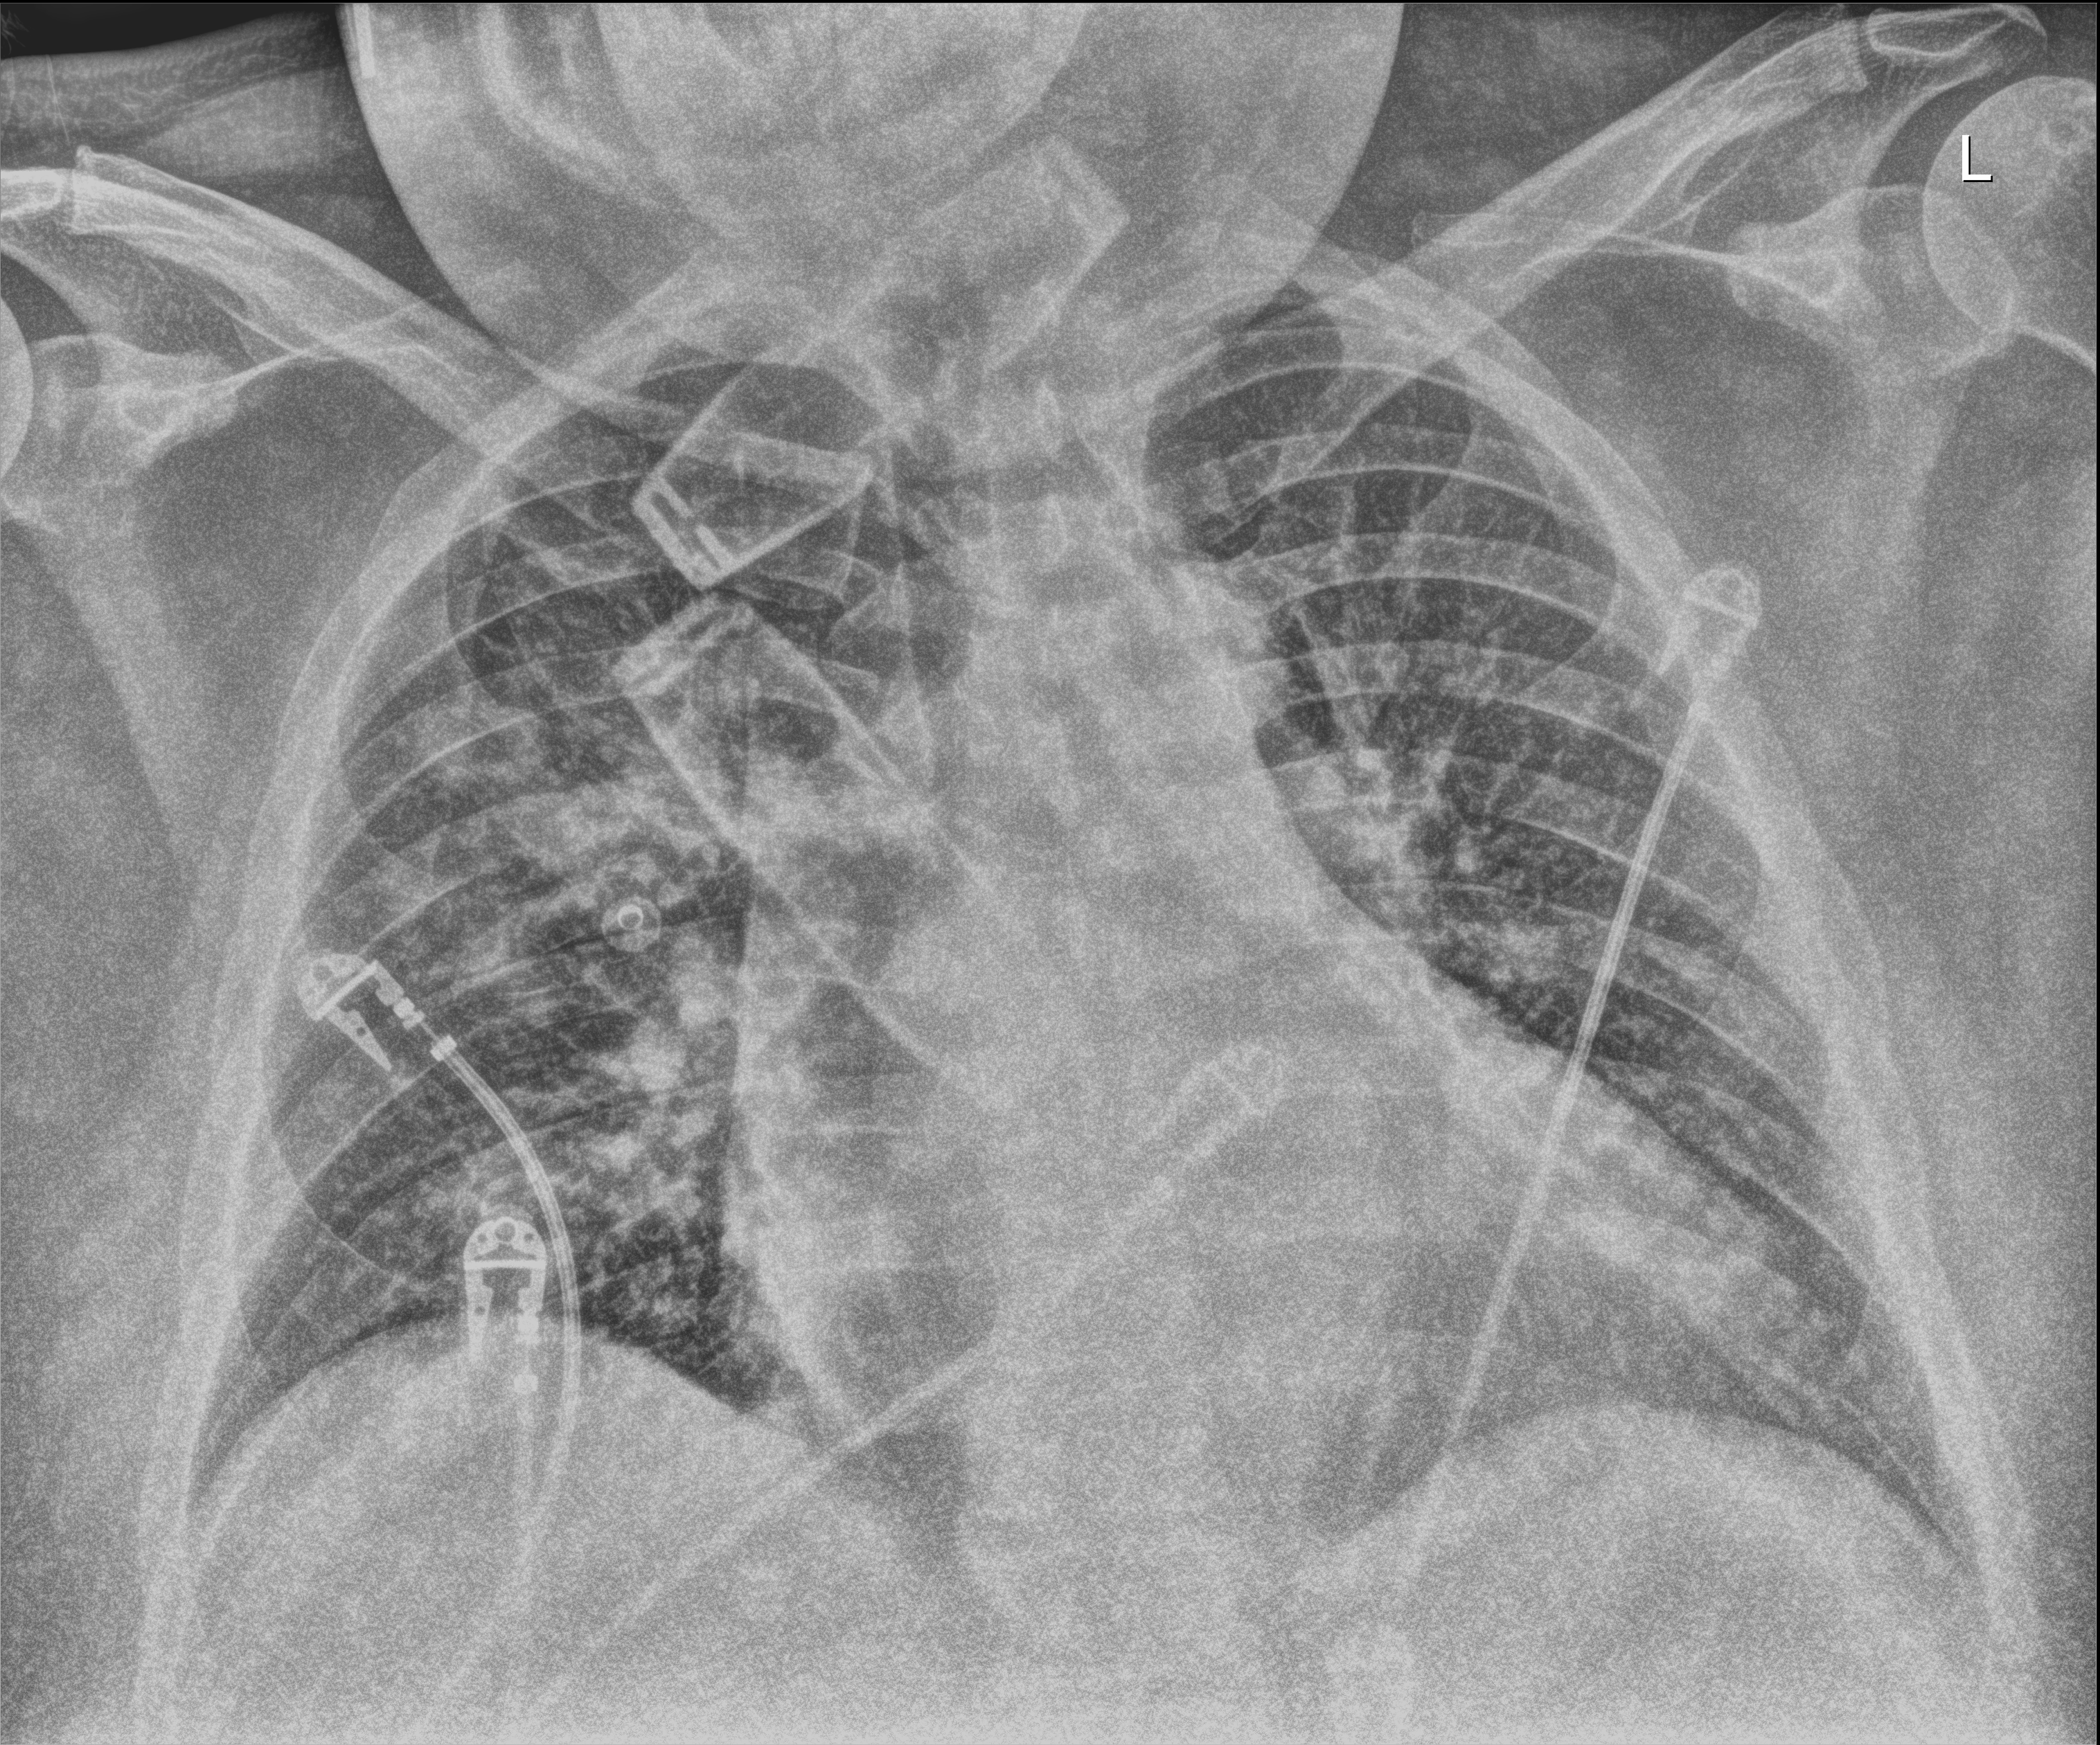
Chest X-ray (portable). Patient hospitalised with COVID-19; male, aged 18–59 years.
From the hospital-stay record, not from the radiograph (when in the stay this image was taken is not recorded): mechanically ventilated during this hospital stay: no; hypertension (admission record): yes; chronic kidney disease (admission record): no.